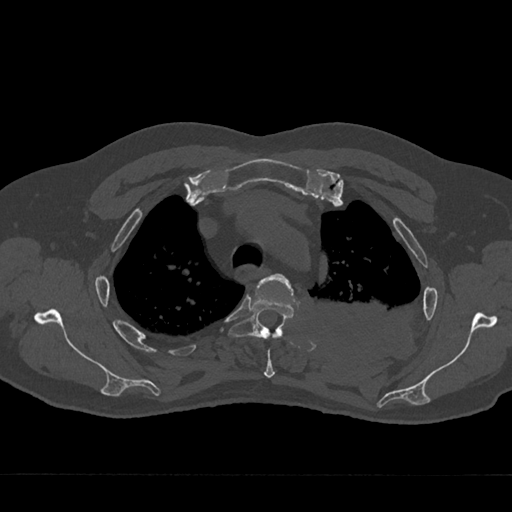
CT including the spine, one axial slice; position 536 of 797 along the scan axis; 120 kVp; bone window (W 1800 / L 400 HU); 0.5 mm slice thickness; 512 × 512 image matrix. Male patient, age 75 years. From the clinical record (not read from this slice): primary cancer: renal; vertebrae with lytic lesions (as recorded): T4.
Annotated regions visible in this slice (semi-automatic segmentation, software-assisted and operator-edited):
- T3 vertebra: bounding box <258,274,294,378> (left, top, right, bottom; pixels)
- T4 vertebra: <228,294,296,339>